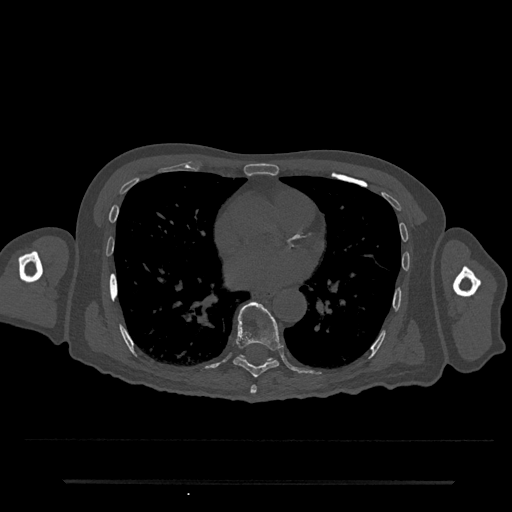
CT including the spine, one axial slice. Position 414 of 797 along the scan axis. Reconstruction kernel Br40s/3. Bone window (W 1800 / L 400 HU). 0.5 mm slice thickness. 512 × 512 image matrix, field of view 427 × 427 mm. Male patient, age 74 years. From the clinical record (not read from this slice): primary cancer: prostate.
Structures marked on this image (semi-automatically segmented with operator editing):
- T7 vertebra: bounding box (x1, y1, x2, y2) in pixels: (250, 385, 257, 394)
- T8 vertebra: (233, 302, 281, 377)
- T9 vertebra: (239, 355, 273, 361)